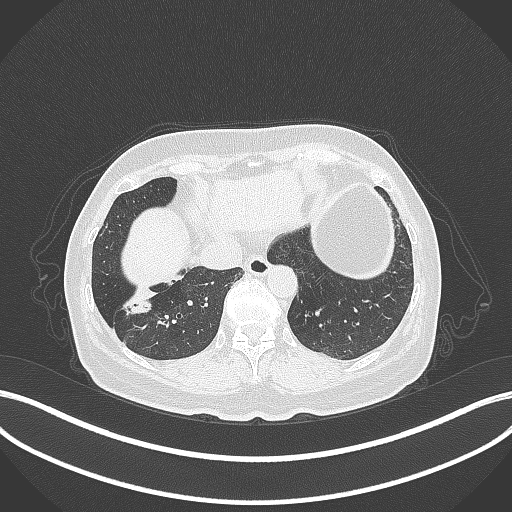
Chest CT, one axial slice. Position 99 of 429 along the scan axis. 120 kVp. Lung window (W 1500 / L -600 HU). 512 × 512 image matrix, field of view 400 × 400 mm. Patient: female, 67 years. From the clinical record (not read from this slice): clinical TNM (as recorded): T1c N1 M0; histopathological grade: G2-3.
Outlined on this slice (rectangle marked by the reading radiologist):
- lung tumour (recorded histology: adenocarcinoma): bounding box (x1, y1, x2, y2) in pixels: (122, 288, 154, 314)